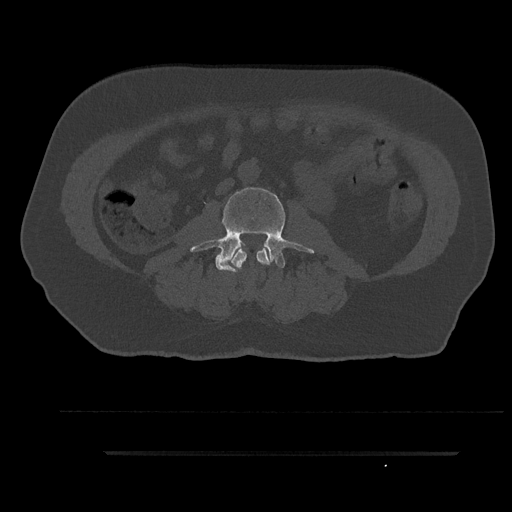
CT including the spine, one axial slice. Slice 61 of 797 in the series (ordered by position). 120 kVp. Bone window (W 1800 / L 400 HU). 512 × 512 image matrix, field of view 432 × 432 mm. Patient: male, 63 years. Case-level facts recorded for this patient, not image findings: primary cancer: renal; vertebrae with lytic lesions (as recorded): T8.
Annotated regions visible in this slice (semi-automatic segmentation, software-assisted and operator-edited):
- L2 vertebra: bounding box (x1, y1, x2, y2) in pixels: (231, 249, 270, 272)
- L3 vertebra: (190, 185, 314, 272)